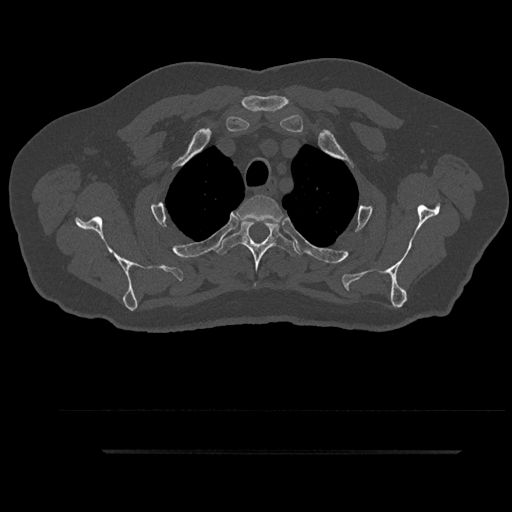
CT including the spine, one axial slice. Slice 729 of 797 in the series (ordered by position). 120 kVp. Bone window (W 1800 / L 400 HU). 0.5 mm slice thickness. 512 × 512 image matrix, field of view 432 × 432 mm. Male patient, age 63 years. Case-level facts recorded for this patient, not image findings: primary cancer: renal; vertebrae with lytic lesions (as recorded): T8.
Structures marked on this image (semi-automatically segmented with operator editing):
- T2 vertebra: bounding box (x1, y1, x2, y2) in pixels: (236, 195, 283, 222)
- T3 vertebra: (215, 219, 301, 288)